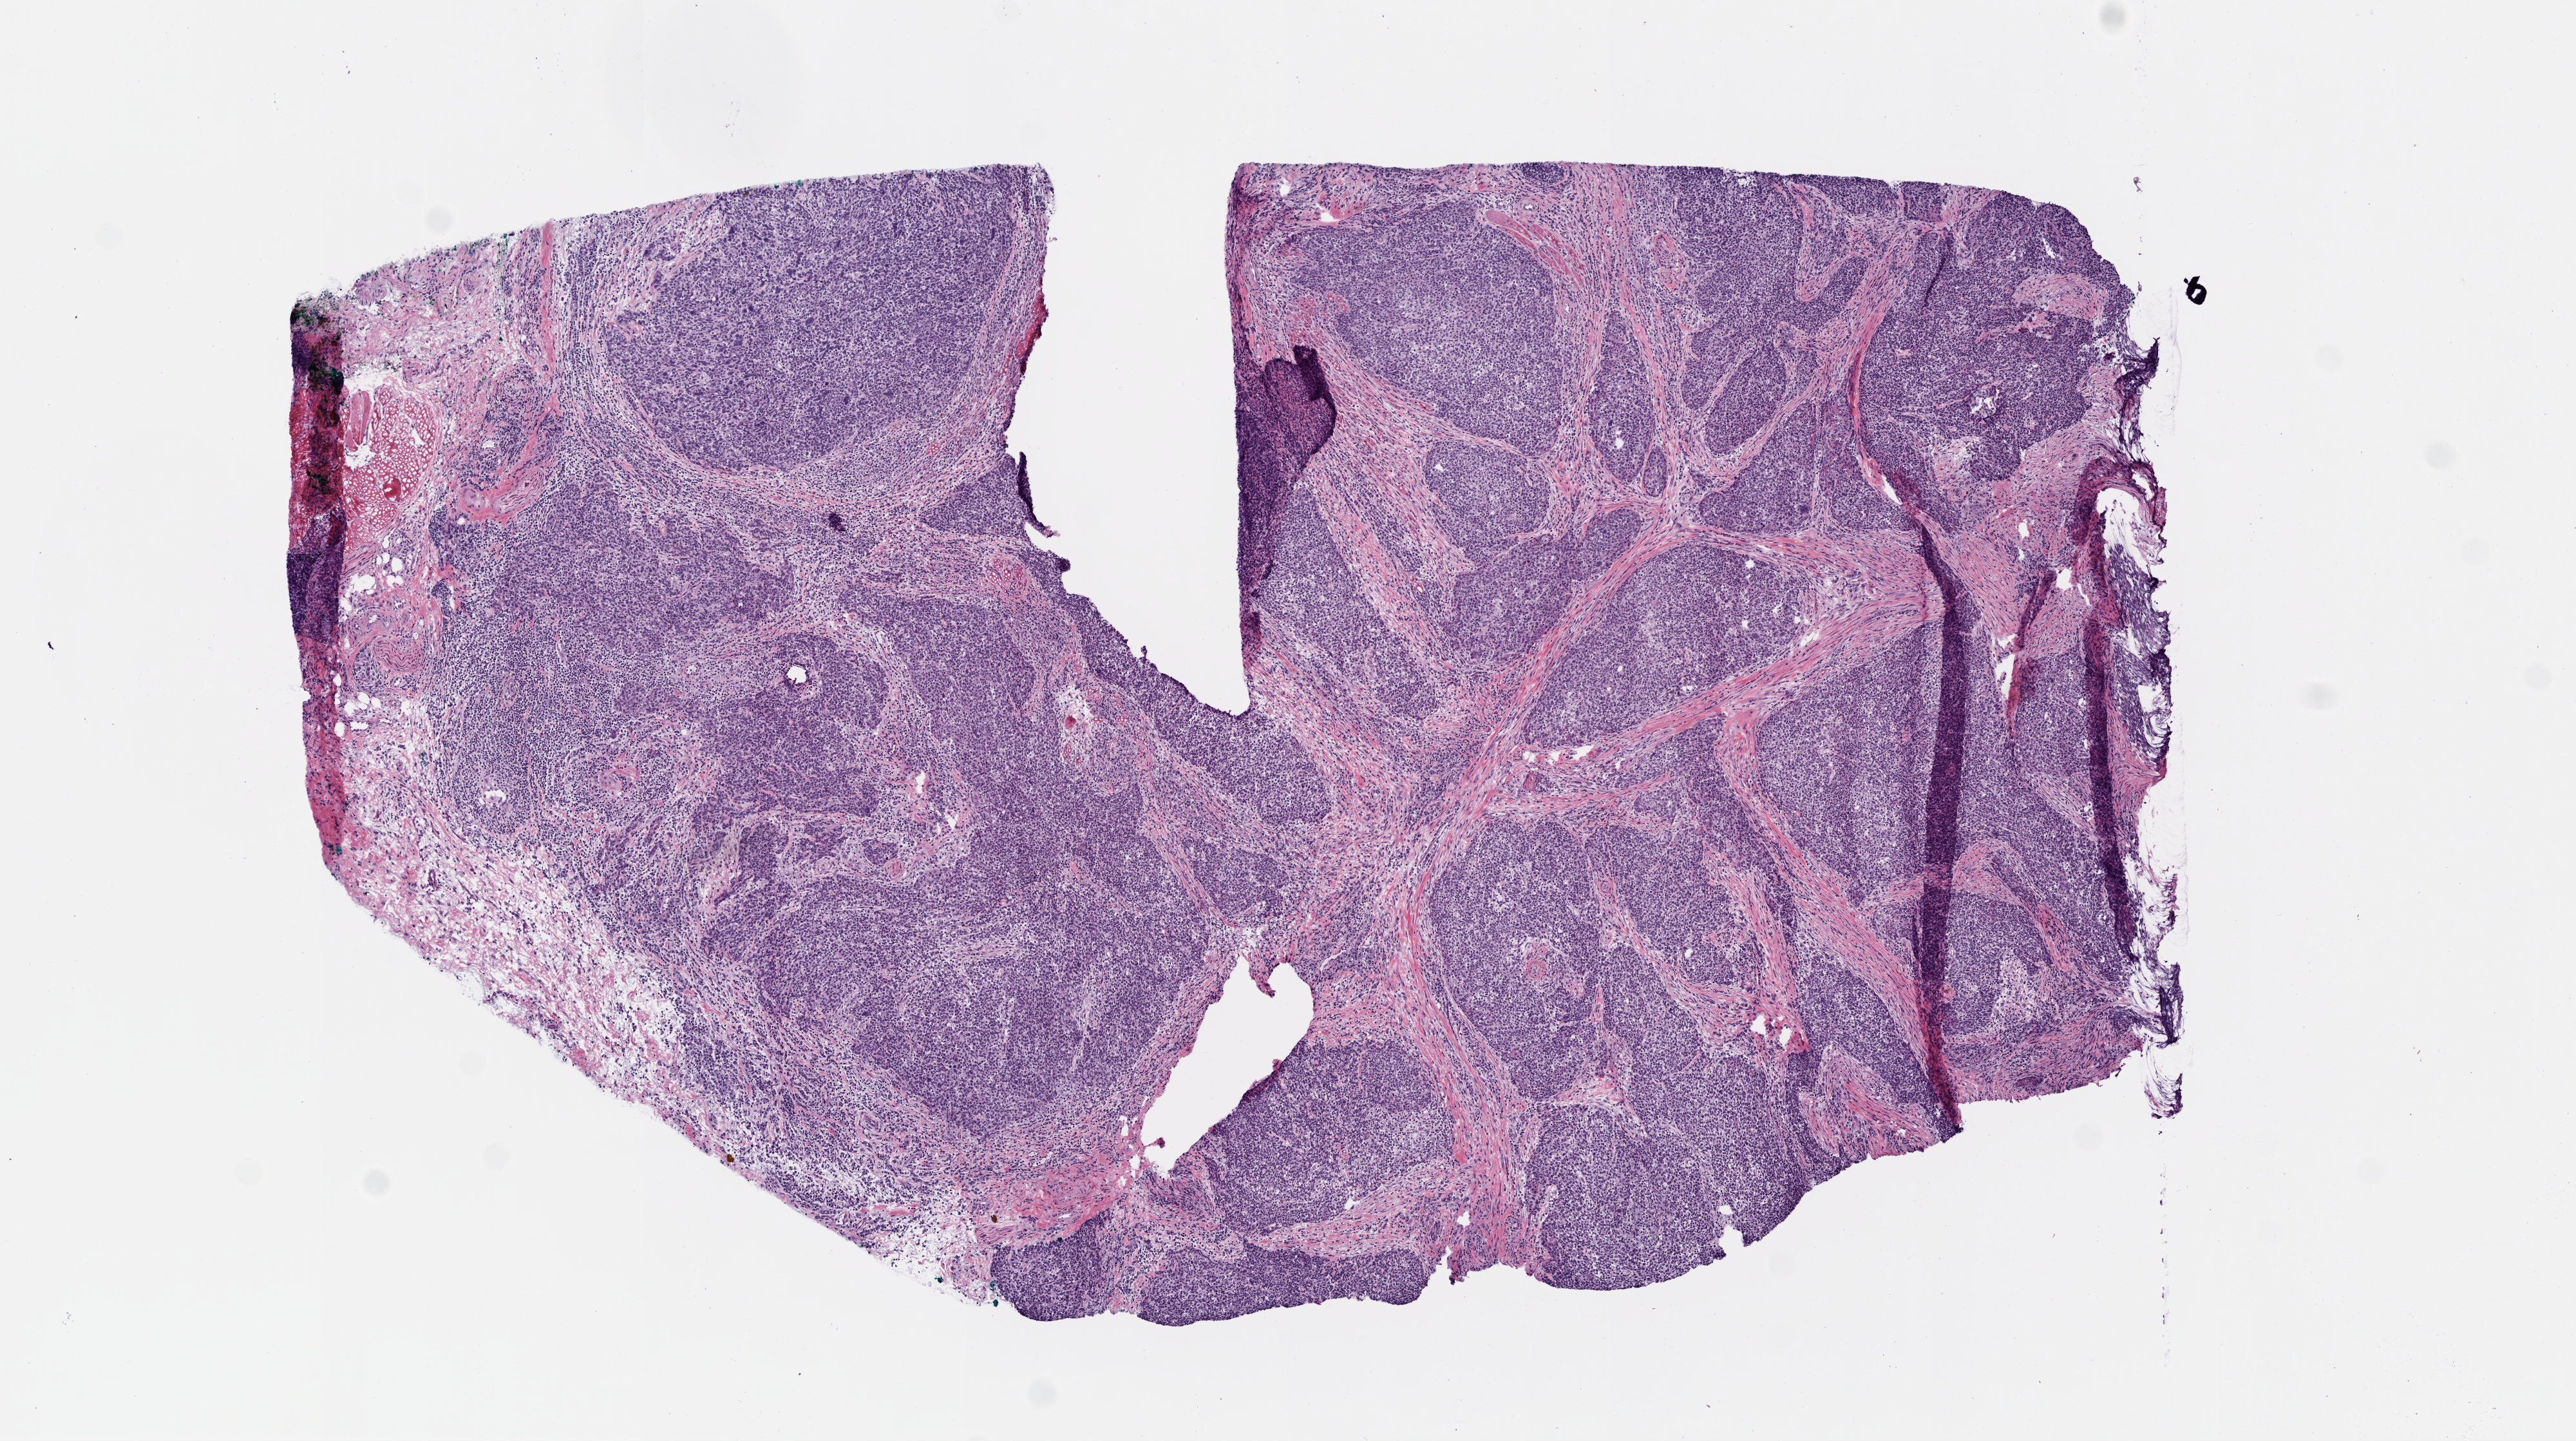
Digitized H&E-stained tissue section (whole slide), low-resolution overview of the scanned area, about 8.0 x 4.5 mm (from a 20x scan). Frozen section. Head and neck, primary tumour sample. Male patient; age at initial diagnosis 71 years. Histologic grade: G3 (poorly differentiated). Pathologist review of this section (percent, as recorded): tumour cells 85%, tumour nuclei 70%, normal cells 0%, stromal cells 15%, necrosis 0%.
* lymph nodes positive (case pathology): 4 of 25 examined
* histologic diagnosis: Squamous cell carcinoma, NOS (tonsil, NOS)